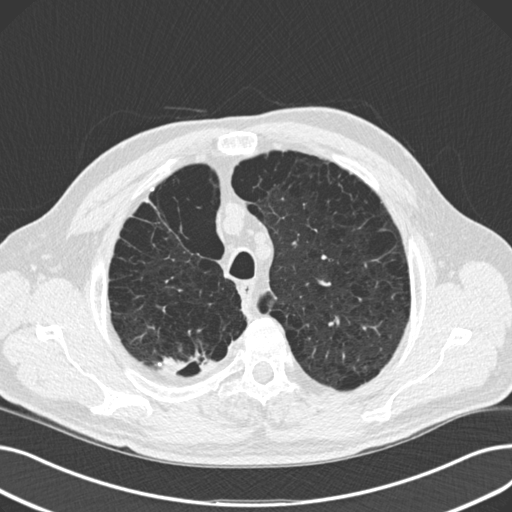
Low-dose screening chest CT, one axial slice. Slice 127 of 165 in the series (ordered by position). Reconstruction kernel B30f. 120 kVp. Lung window (W 1500 / L -600 HU). 2 mm slice thickness. 512 × 512 image matrix.
Outlined on this slice (expert manual segmentation):
- lesion 2 (tumor, upper lobe of right lung): bounding box <163,357,188,374> (left, top, right, bottom; pixels)